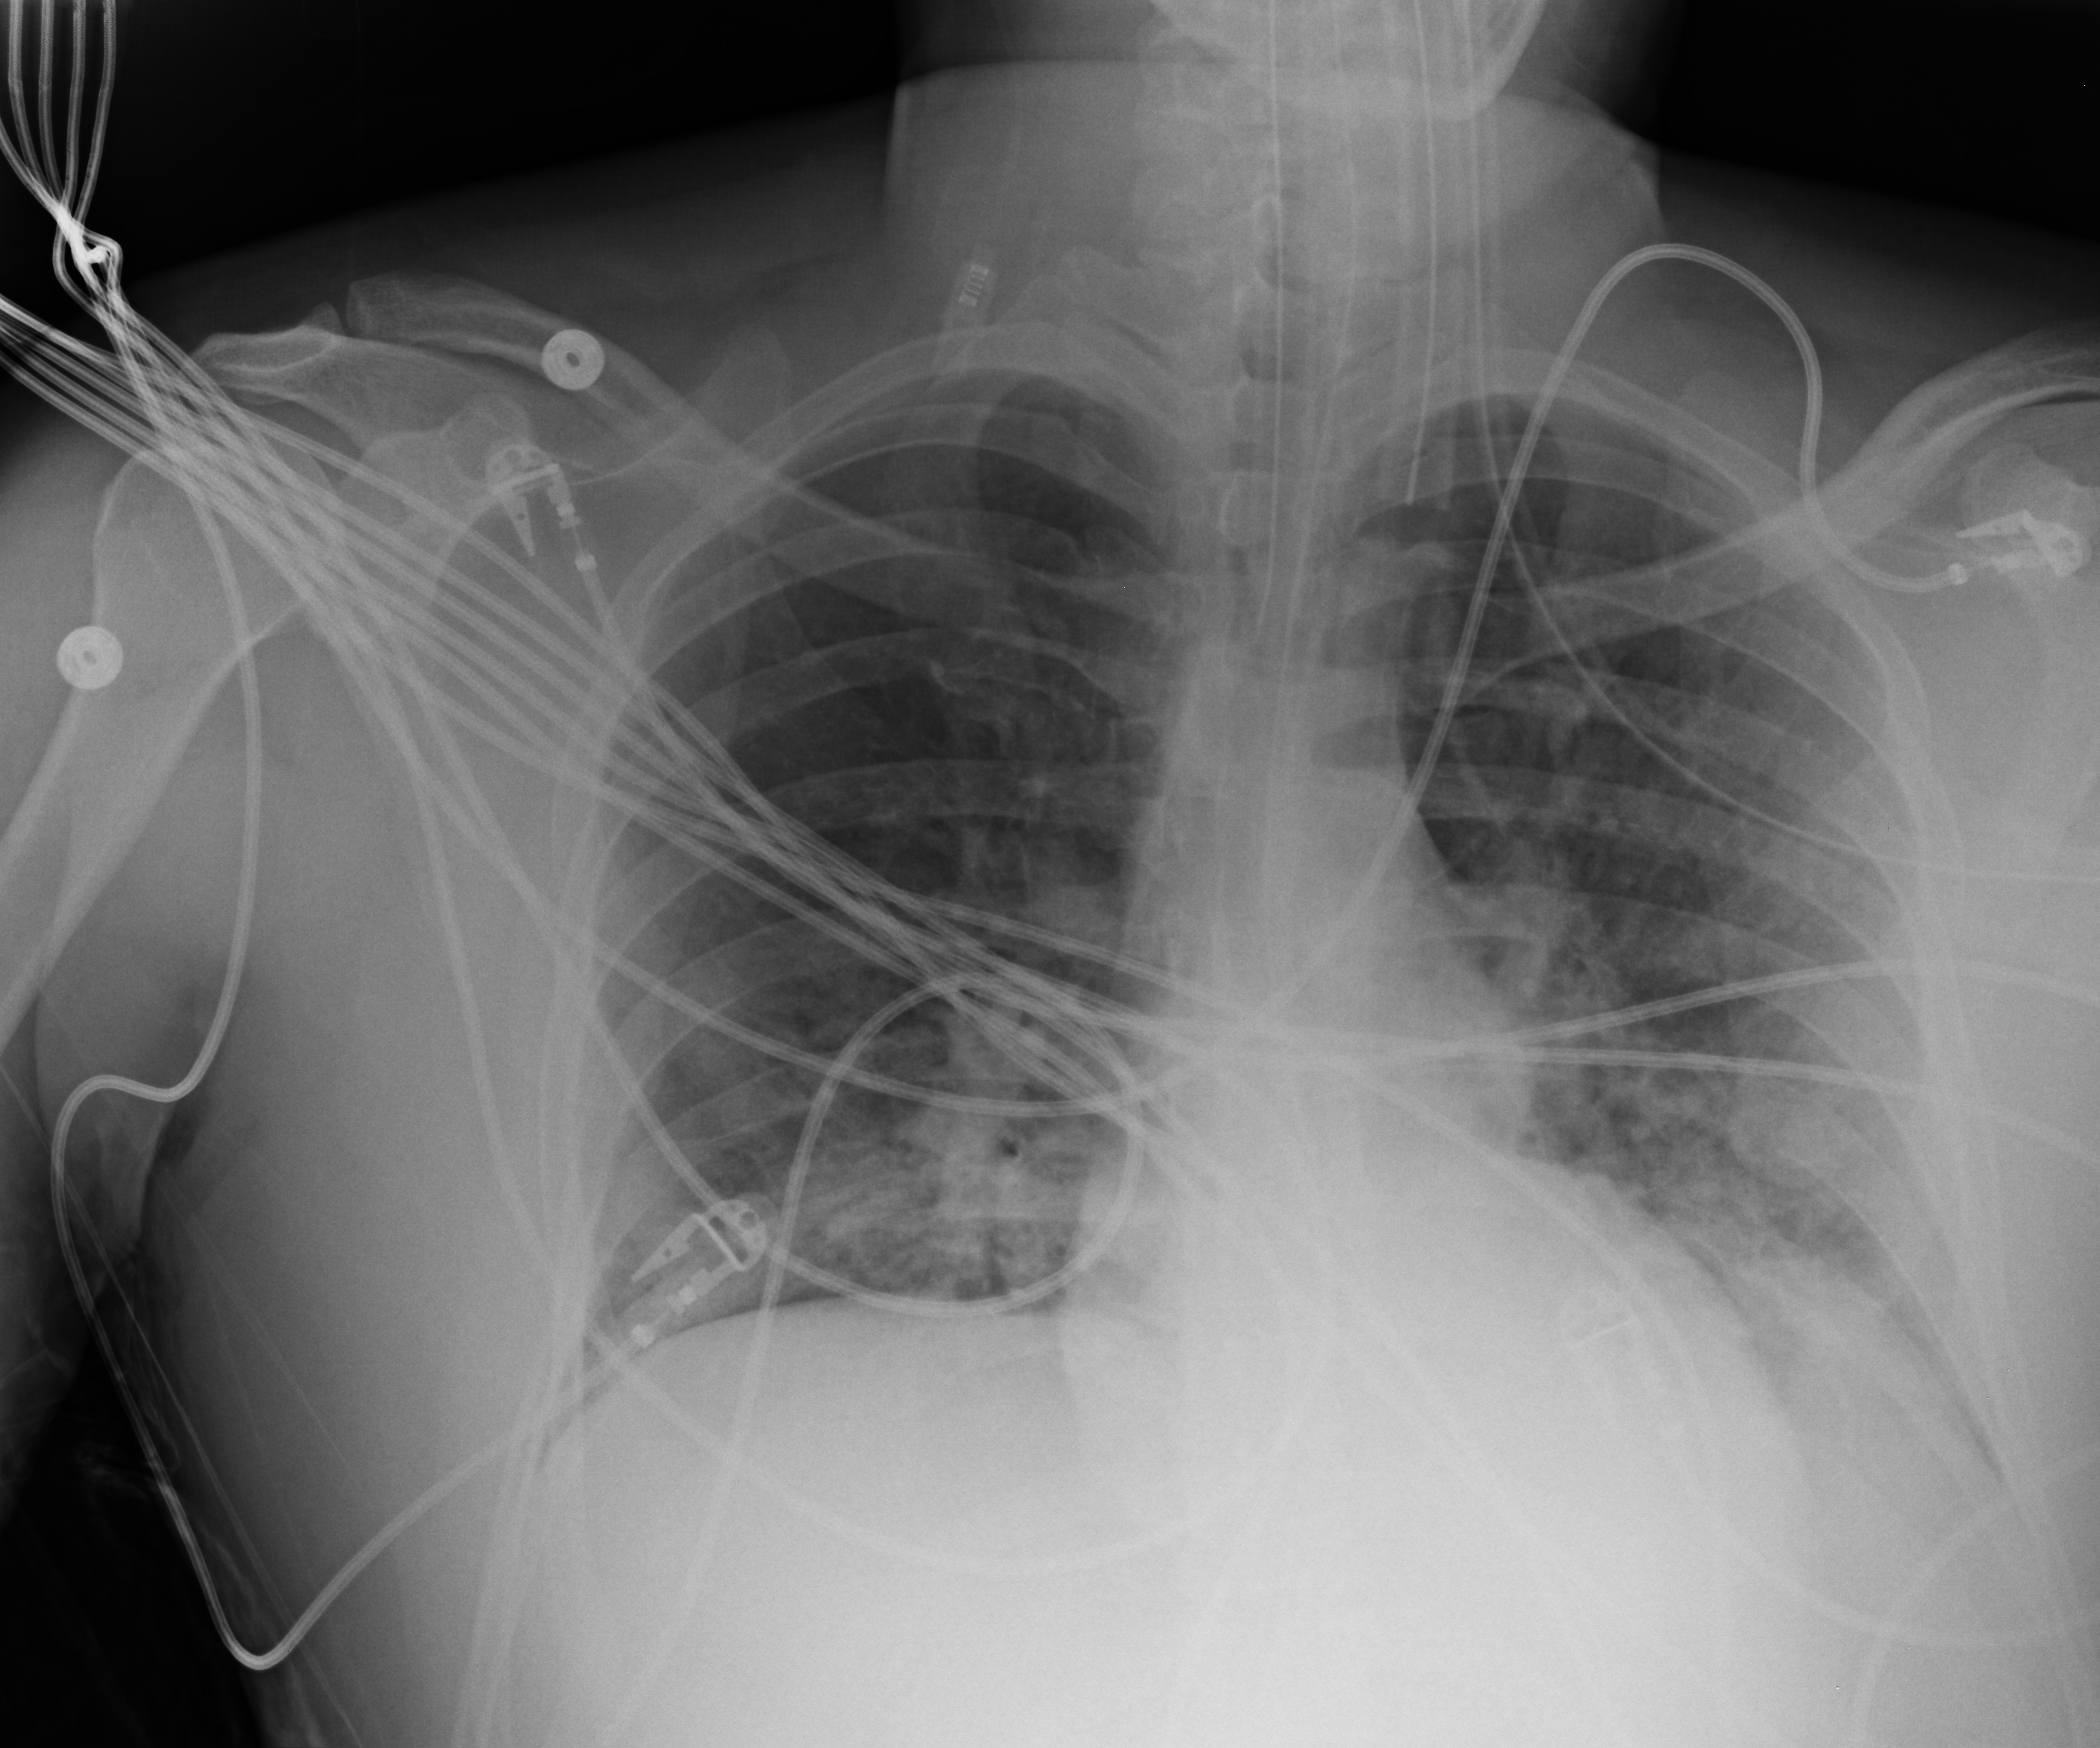
Bedside chest radiograph (computed radiography); anteroposterior (AP) projection. Patient hospitalised with COVID-19; male, aged 18–59 years.
From the hospital-stay record, not from the radiograph (when in the stay this image was taken is not recorded):
- length of hospital stay: 22 days